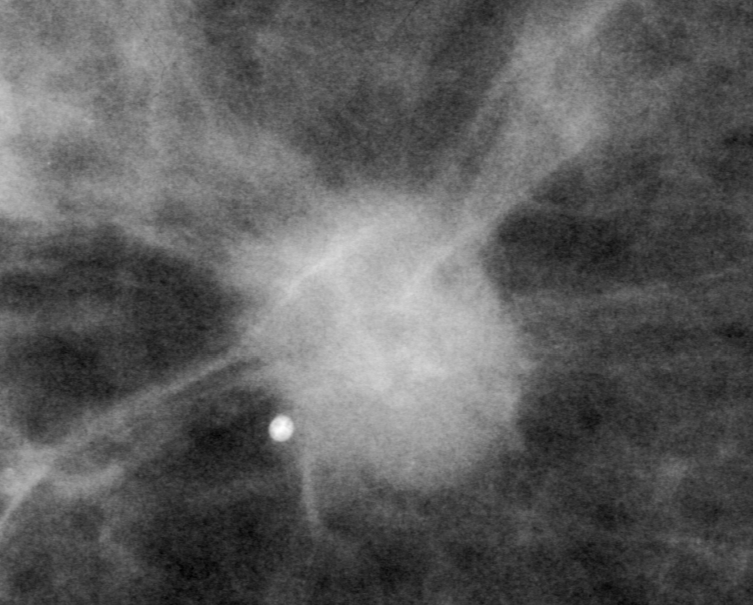
Region of interest cut from a scanned film mammogram (one marked finding), left breast, CC view, BI-RADS breast density category 1 (scale 1–4).
- Finding: mass, shape oval, margins spiculated; BI-RADS assessment category 5; subtlety rating 5 on a 1 (subtle) to 5 (obvious) scale; pathology result (as recorded, not read from the image): malignant.